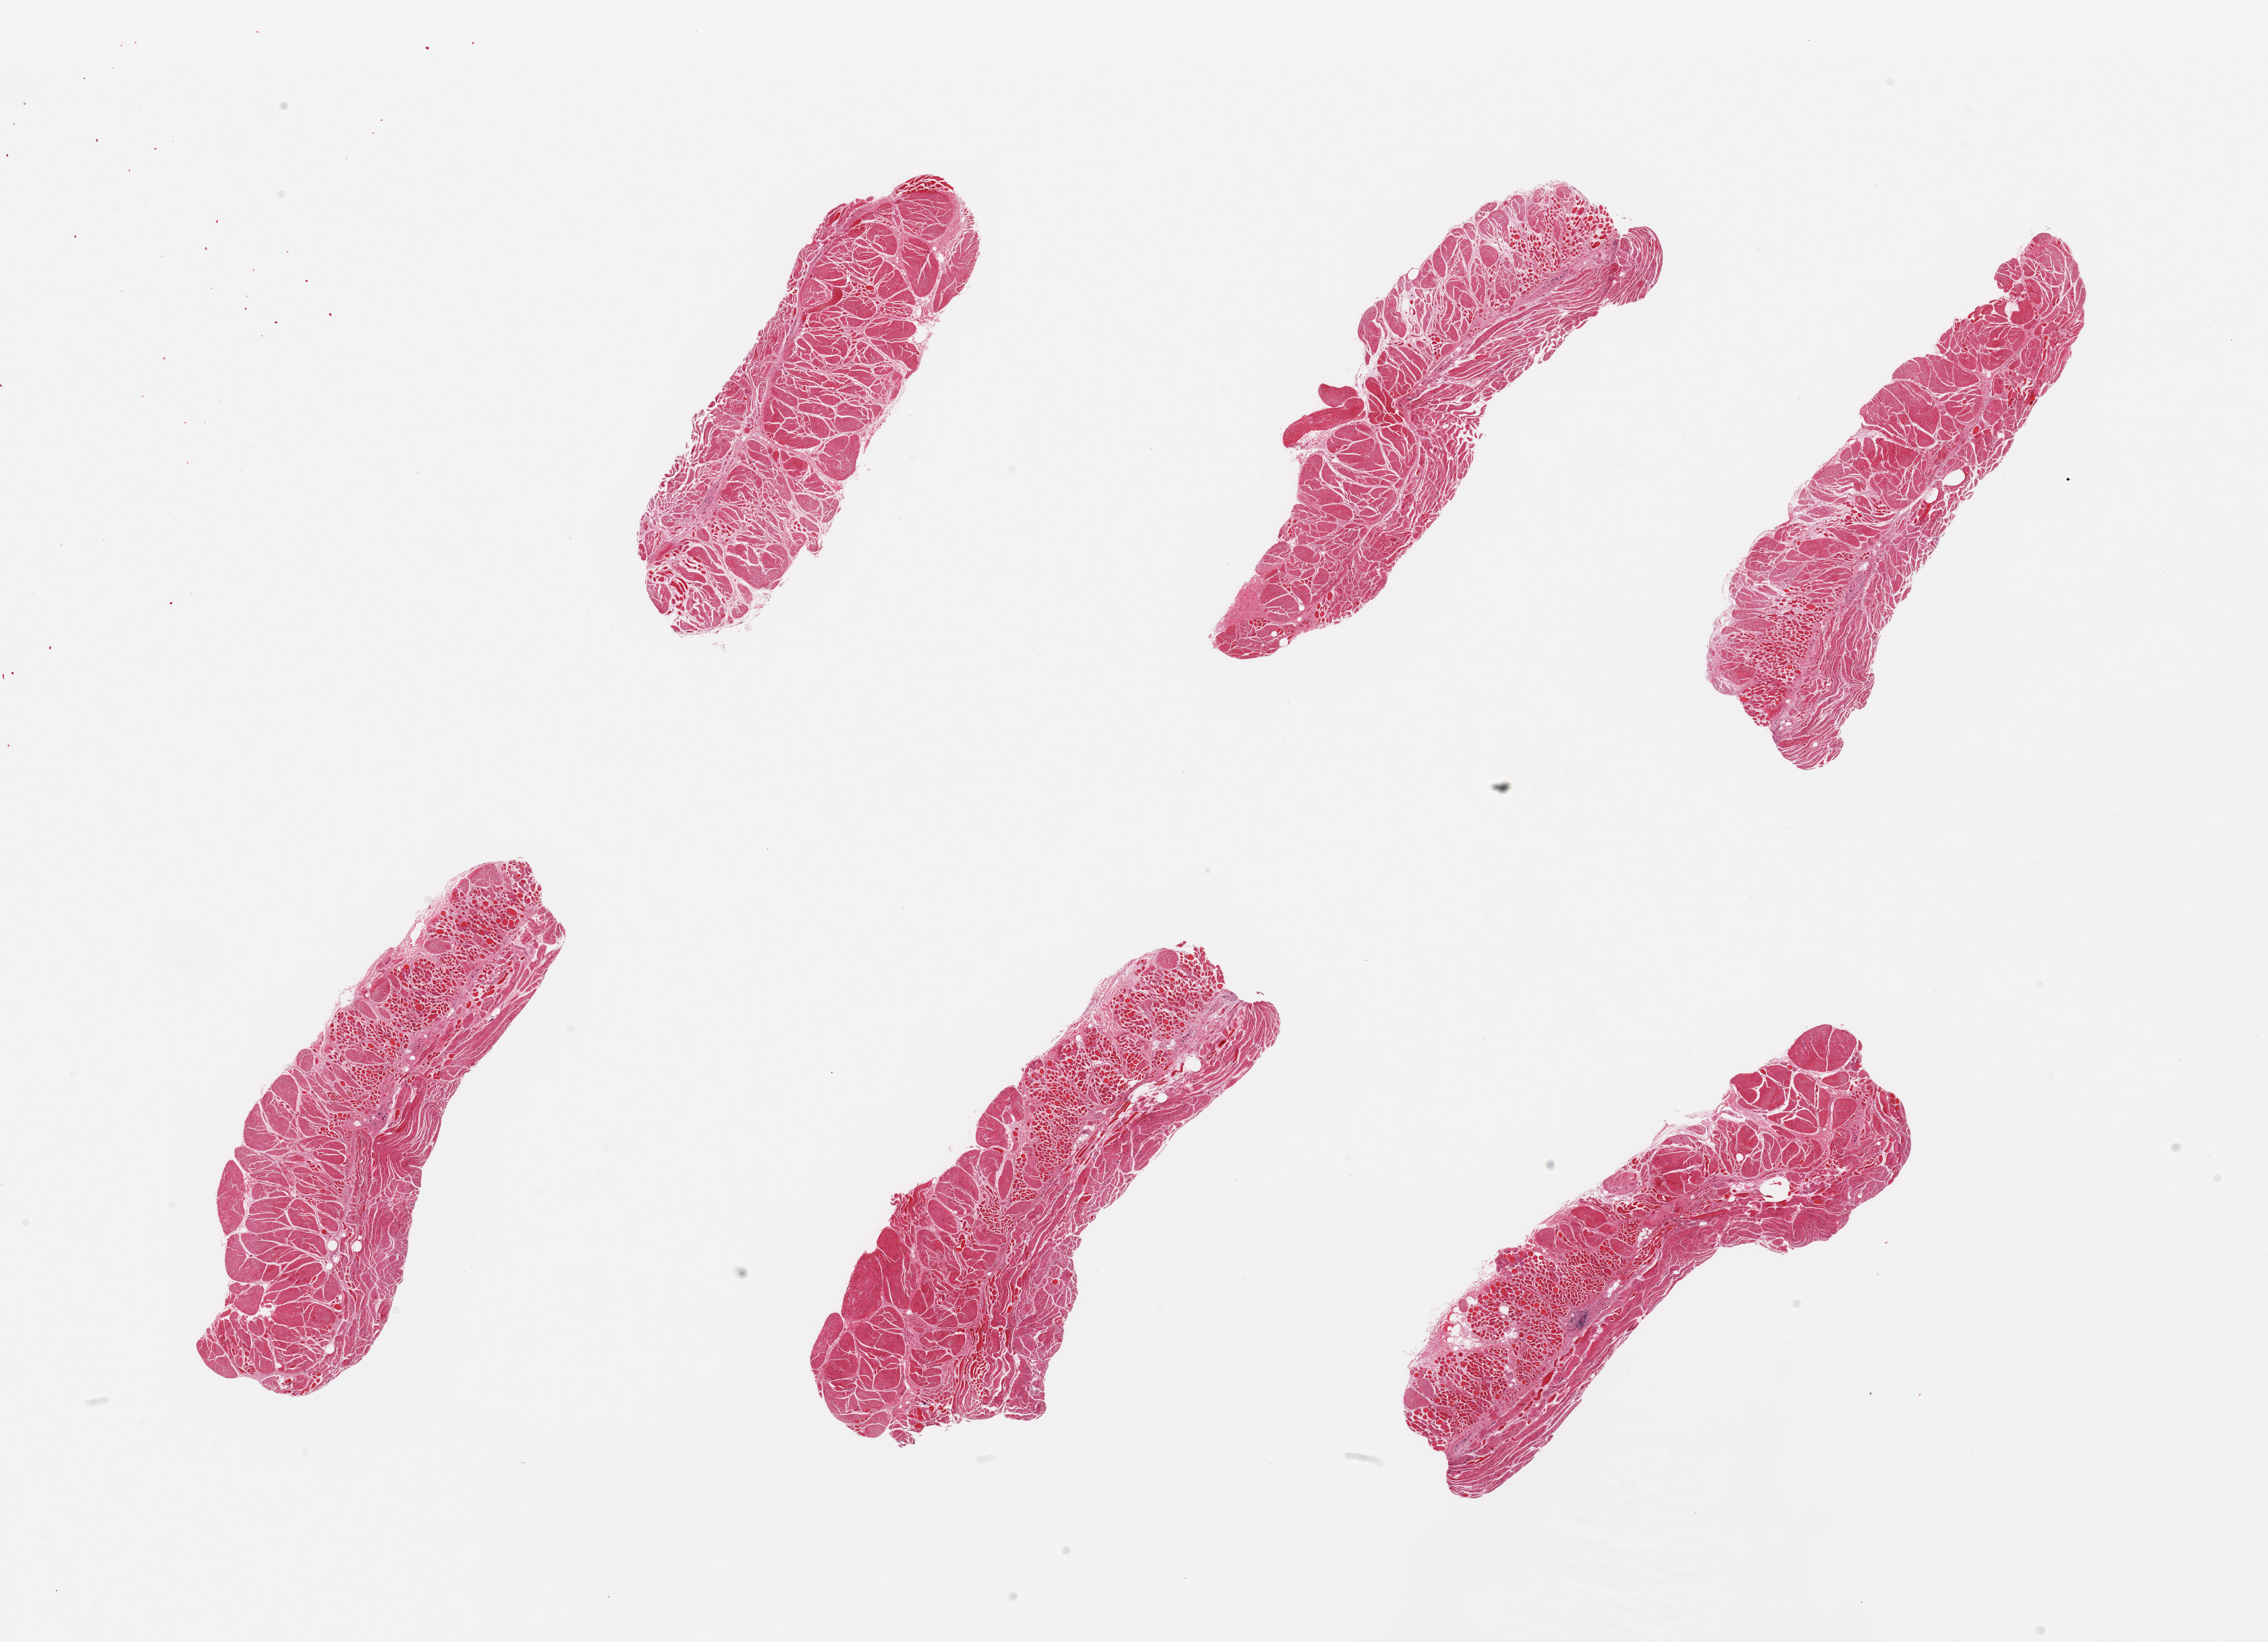
Whole-slide image, H&E stain, shown as a low-resolution overview of the whole scanned area (about 26.6 x 19.2 mm, from a 20x scan), PAXgene-fixed, paraffin-embedded tissue, target tissue: esophageal muscle, donor tissue sample.
• pathologist's review note for this sample: 6 pieces, well trimmed, admixture of skeletal and smooth muscle indicating sample of upper esophagus